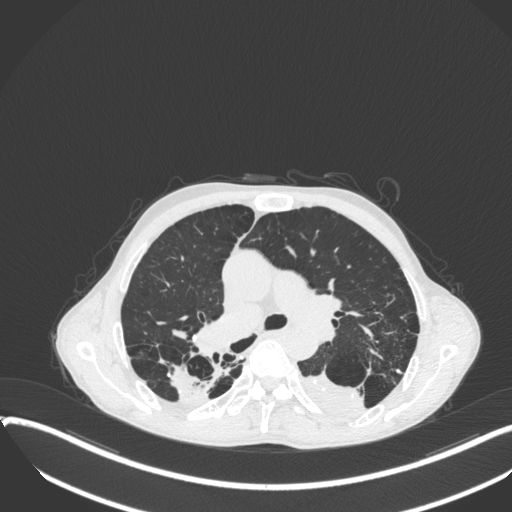
Chest CT, one axial slice. Position 242 of 400 along the scan axis. Lung window (W 1500 / L -600 HU). 512 × 512 image matrix, field of view 400 × 400 mm. Male patient, age 57 years. Case-level facts recorded for this patient, not image findings: clinical TNM (as recorded): T4 N0 M0.
Outlined on this slice (rectangle marked by the reading radiologist):
- lung tumour (recorded histology: squamous cell carcinoma): box from (x=297, y=364) to (x=371, y=420) px